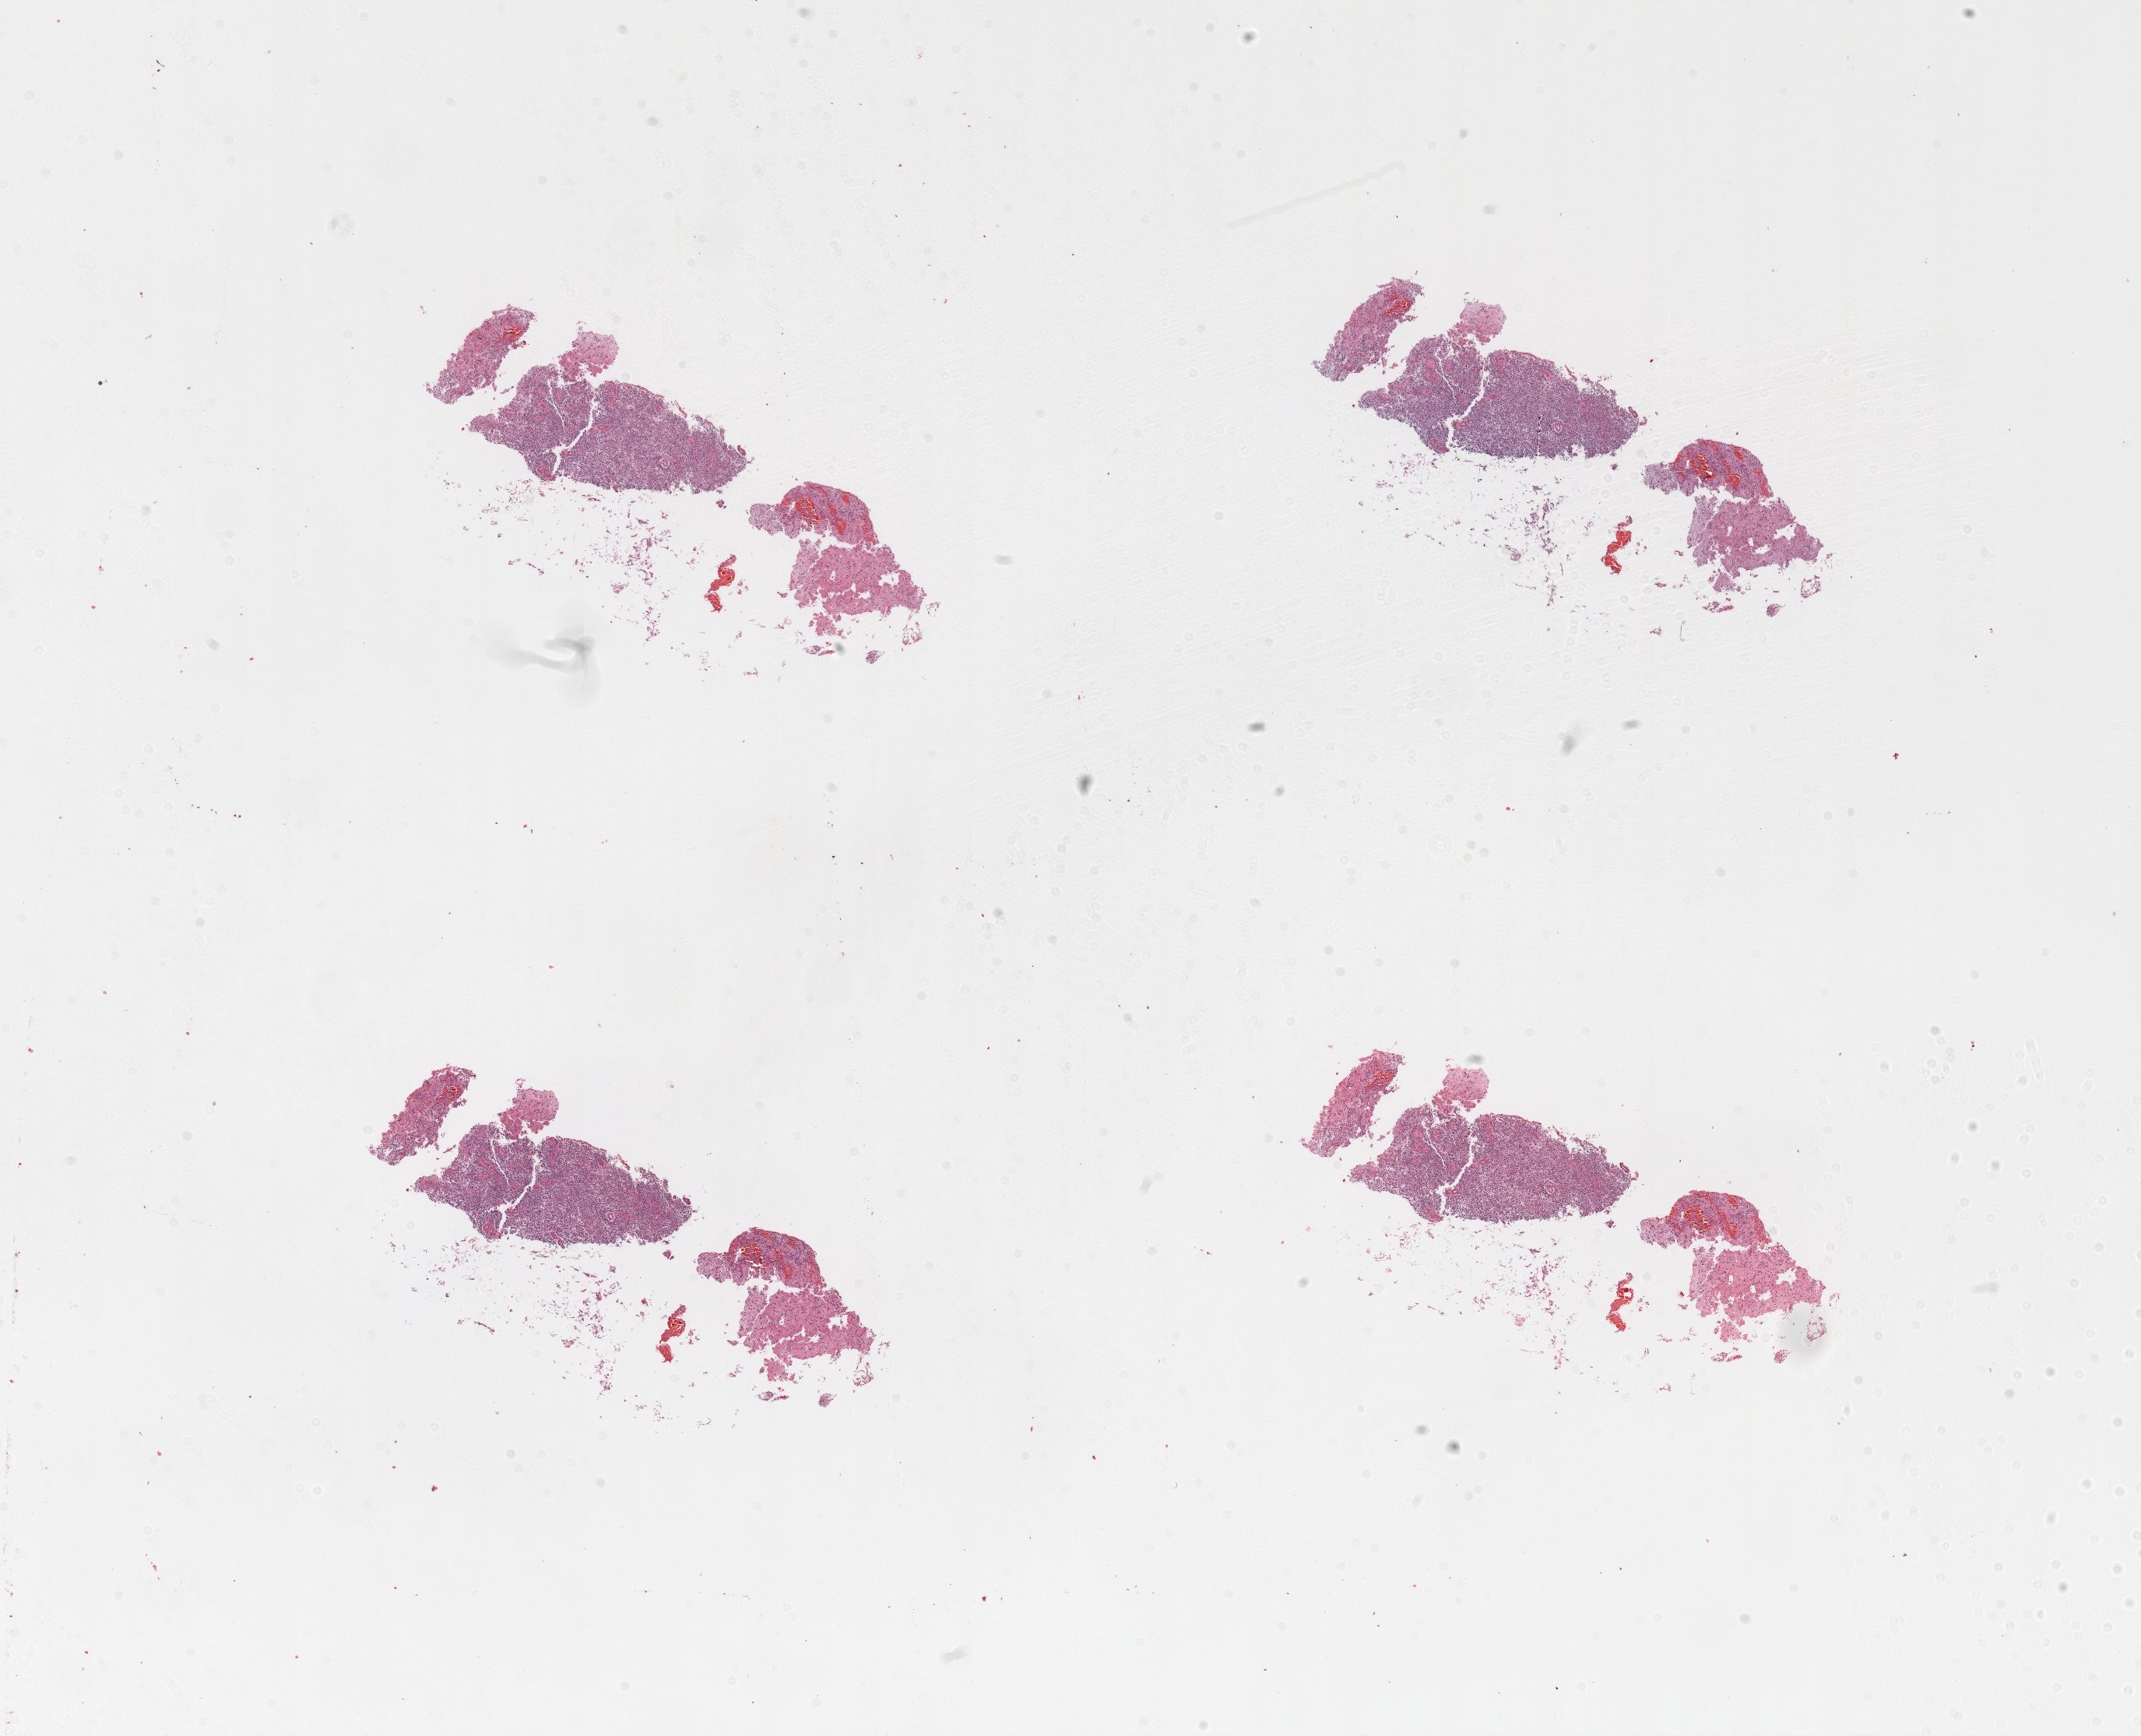
Digitized H&E tissue section (whole slide), a low-resolution overview of the entire scanned area, about 22.1 x 17.9 mm (from a 20x scan). Formalin-fixed paraffin-embedded (FFPE) diagnostic section. Sample: primary tumour, brain. Female, age 65 years at initial diagnosis.
* histologic diagnosis: Glioblastoma